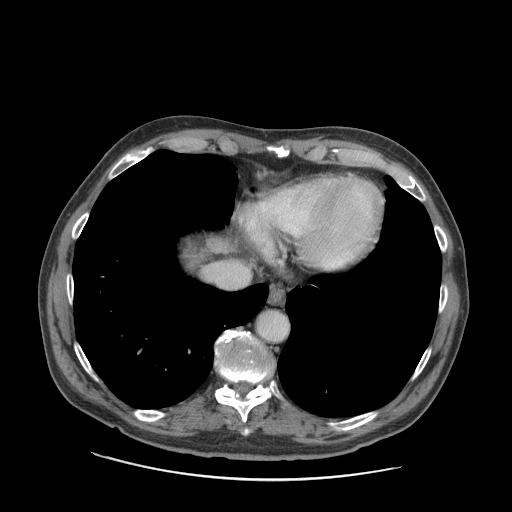
Contrast-enhanced abdominal CT (liver protocol), one axial slice; position 81 of 89 along the scan axis; 140 kVp; soft-tissue window (W 400 / L 40 HU); 2.5 mm slice thickness; 512 × 512 image matrix, field of view 420 × 420 mm. From the clinical record (not read from this slice): diagnosis: hepatocellular carcinoma (patient treated with transarterial chemoembolisation; whether this scan precedes or follows treatment is not stated here); TNM stage (as recorded): Stage-I; Child-Pugh class: A; tumour differentiation: moderately differentiated; tumour nodularity: uninodular.
Outlined on this slice (semi-automatically segmented with operator editing):
- liver parenchyma outside the tumour (the mass and vessels are separate outlines, so this box may not span the whole liver): box from (x=184, y=238) to (x=228, y=266) px